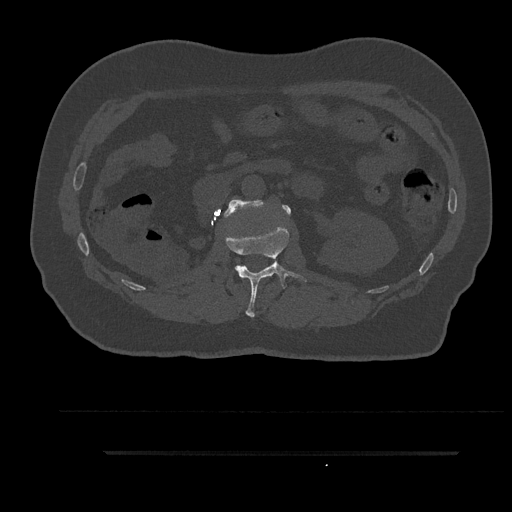
CT including the spine, one axial slice; position 160 of 797 along the scan axis; reconstruction kernel Br40s/3; bone window (W 1800 / L 400 HU); 512 × 512 image matrix, field of view 432 × 432 mm. Male patient, age 63 years. From the clinical record (not read from this slice): primary cancer: renal.
Structures marked on this image (semi-automatically segmented with operator editing):
- L1 vertebra: box from (x=225, y=226) to (x=306, y=318) px
- L2 vertebra: (x=224, y=199)–(x=291, y=217)